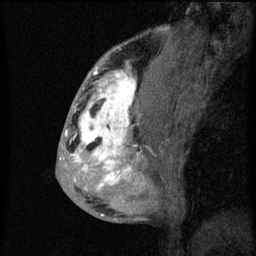
Breast MRI (dynamic contrast-enhanced), one sagittal slice. Position 25 of 60 along the scan axis. Dynamic contrast-enhanced series, image 2 of 3 at this slice position (ordered by acquisition). 1.5 T. TE 4.2 ms, TR 8 ms. 2 mm slice thickness. 256 × 256 image matrix, field of view 180 × 180 mm. Female patient, age 50 years.
Outlined on this slice (semi-automatic segmentation, software-assisted and operator-edited):
- analysis volume of interest (the breast-tissue region the enhancement analysis was run in; not a lesion): bounding box (x1, y1, x2, y2) in pixels: (66, 64, 141, 187)
- tumour enhancement mask (voxels above the 70 % enhancement threshold inside the analysis volume of interest): (66, 68, 139, 187)